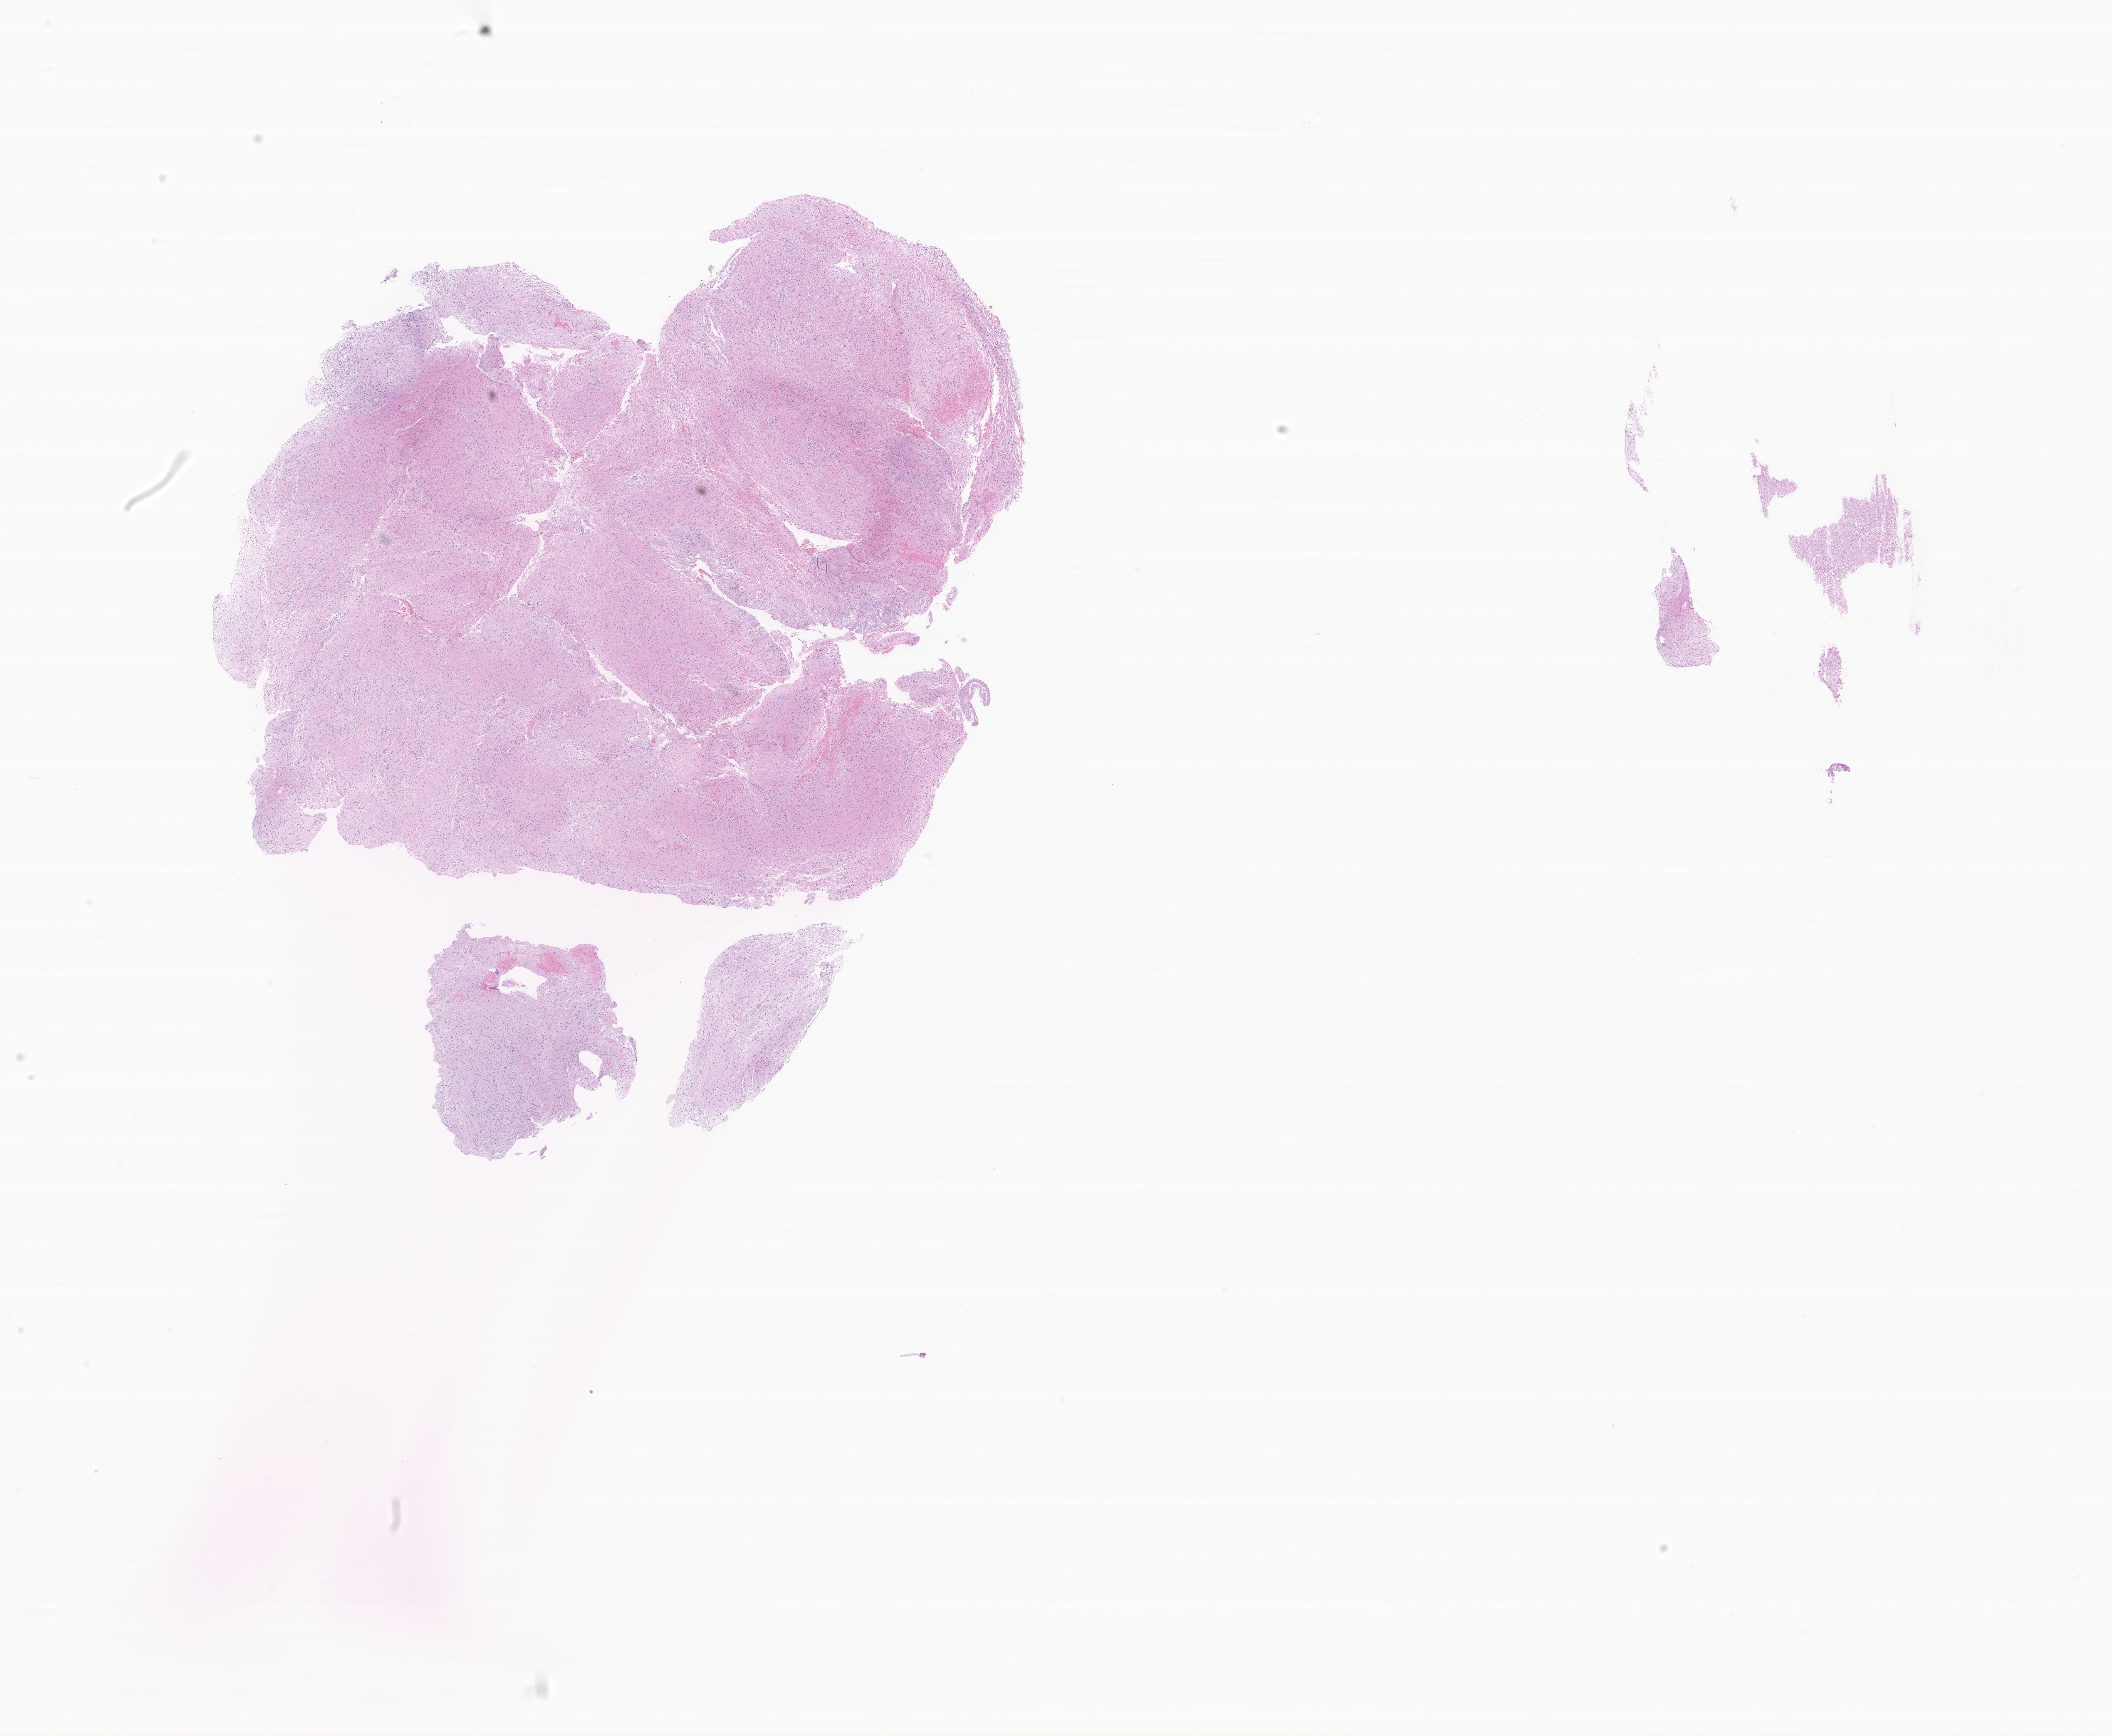
Whole-slide image, H&E stain of tumor tissue from the spinal cord — a low-resolution overview of the entire scanned area, about 21.4 x 17.6 mm, FFPE section. Patient female; age 133 months (11 years 1 month).
Diagnosis (ICD-O-3 morphology term): Glioma, malignant.